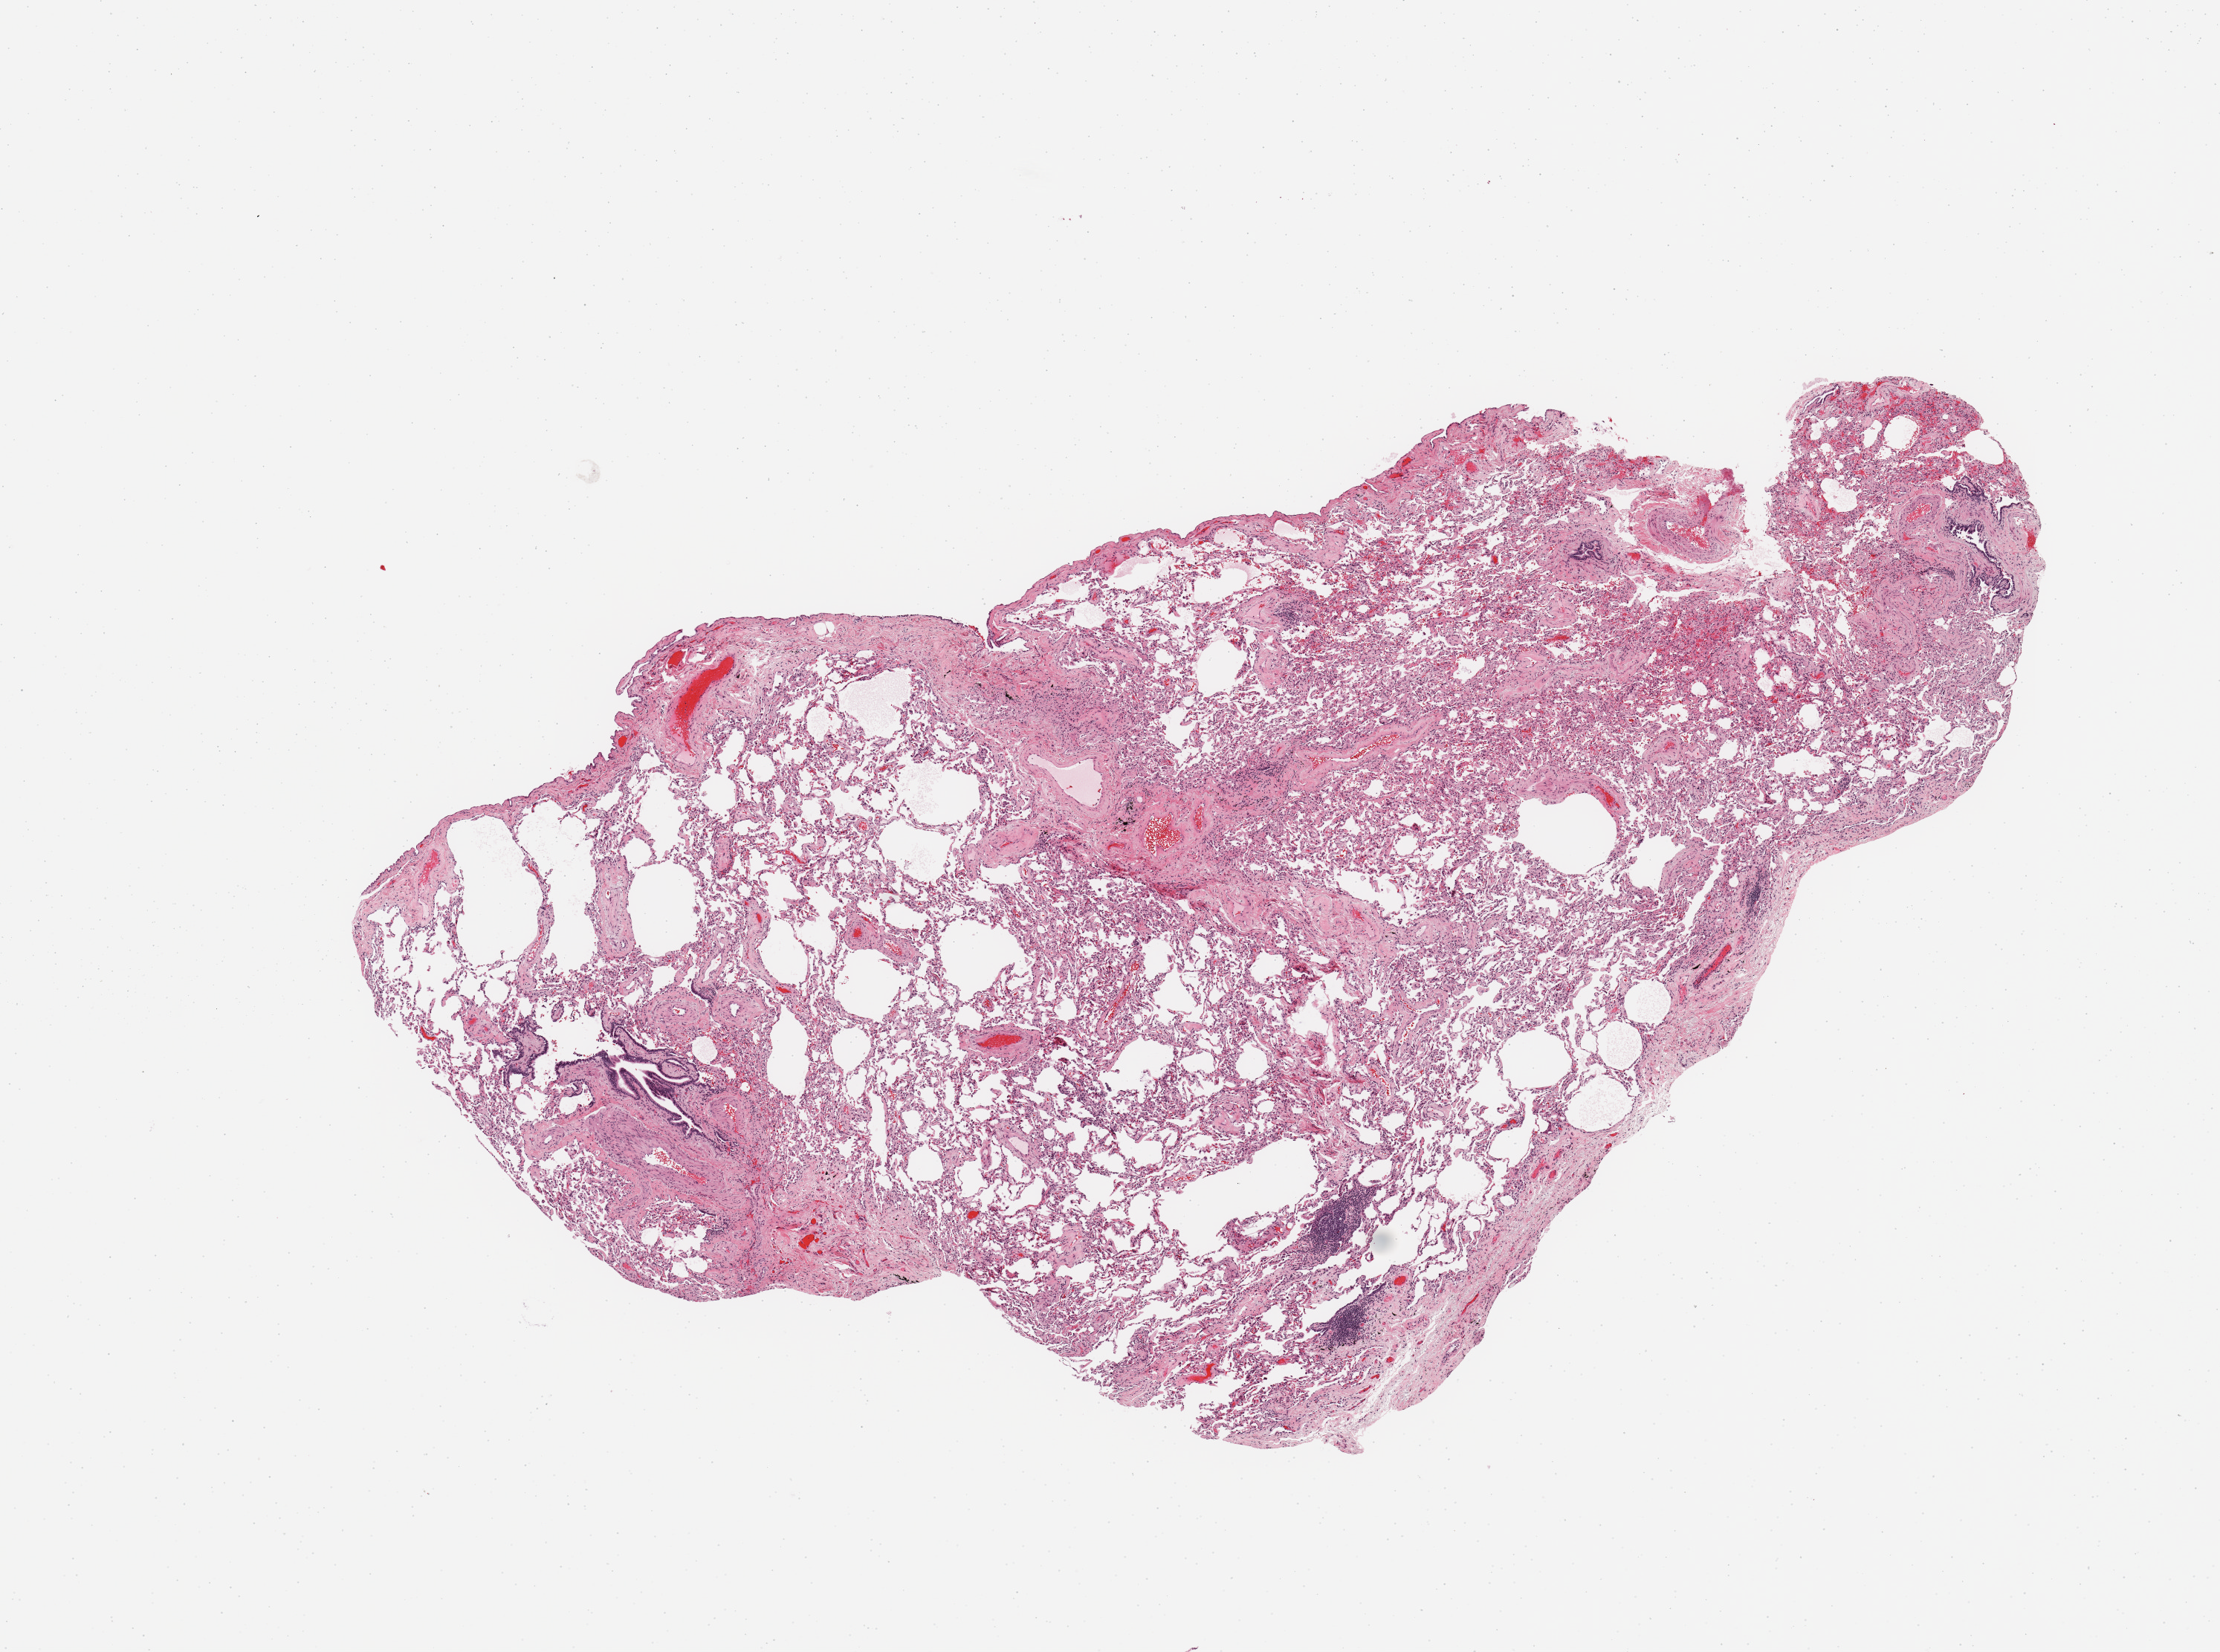
Hematoxylin and eosin (H&E) stained whole-slide image, whole scanned area (about 11.8 x 8.8 mm) shown as a low-resolution overview, normal (non-tumour) tissue sample, lung. Patient: male, age 81 years.
This section: normal (non-tumour) tissue from the same patient. Patient diagnosis: Adenocarcinoma, NOS.